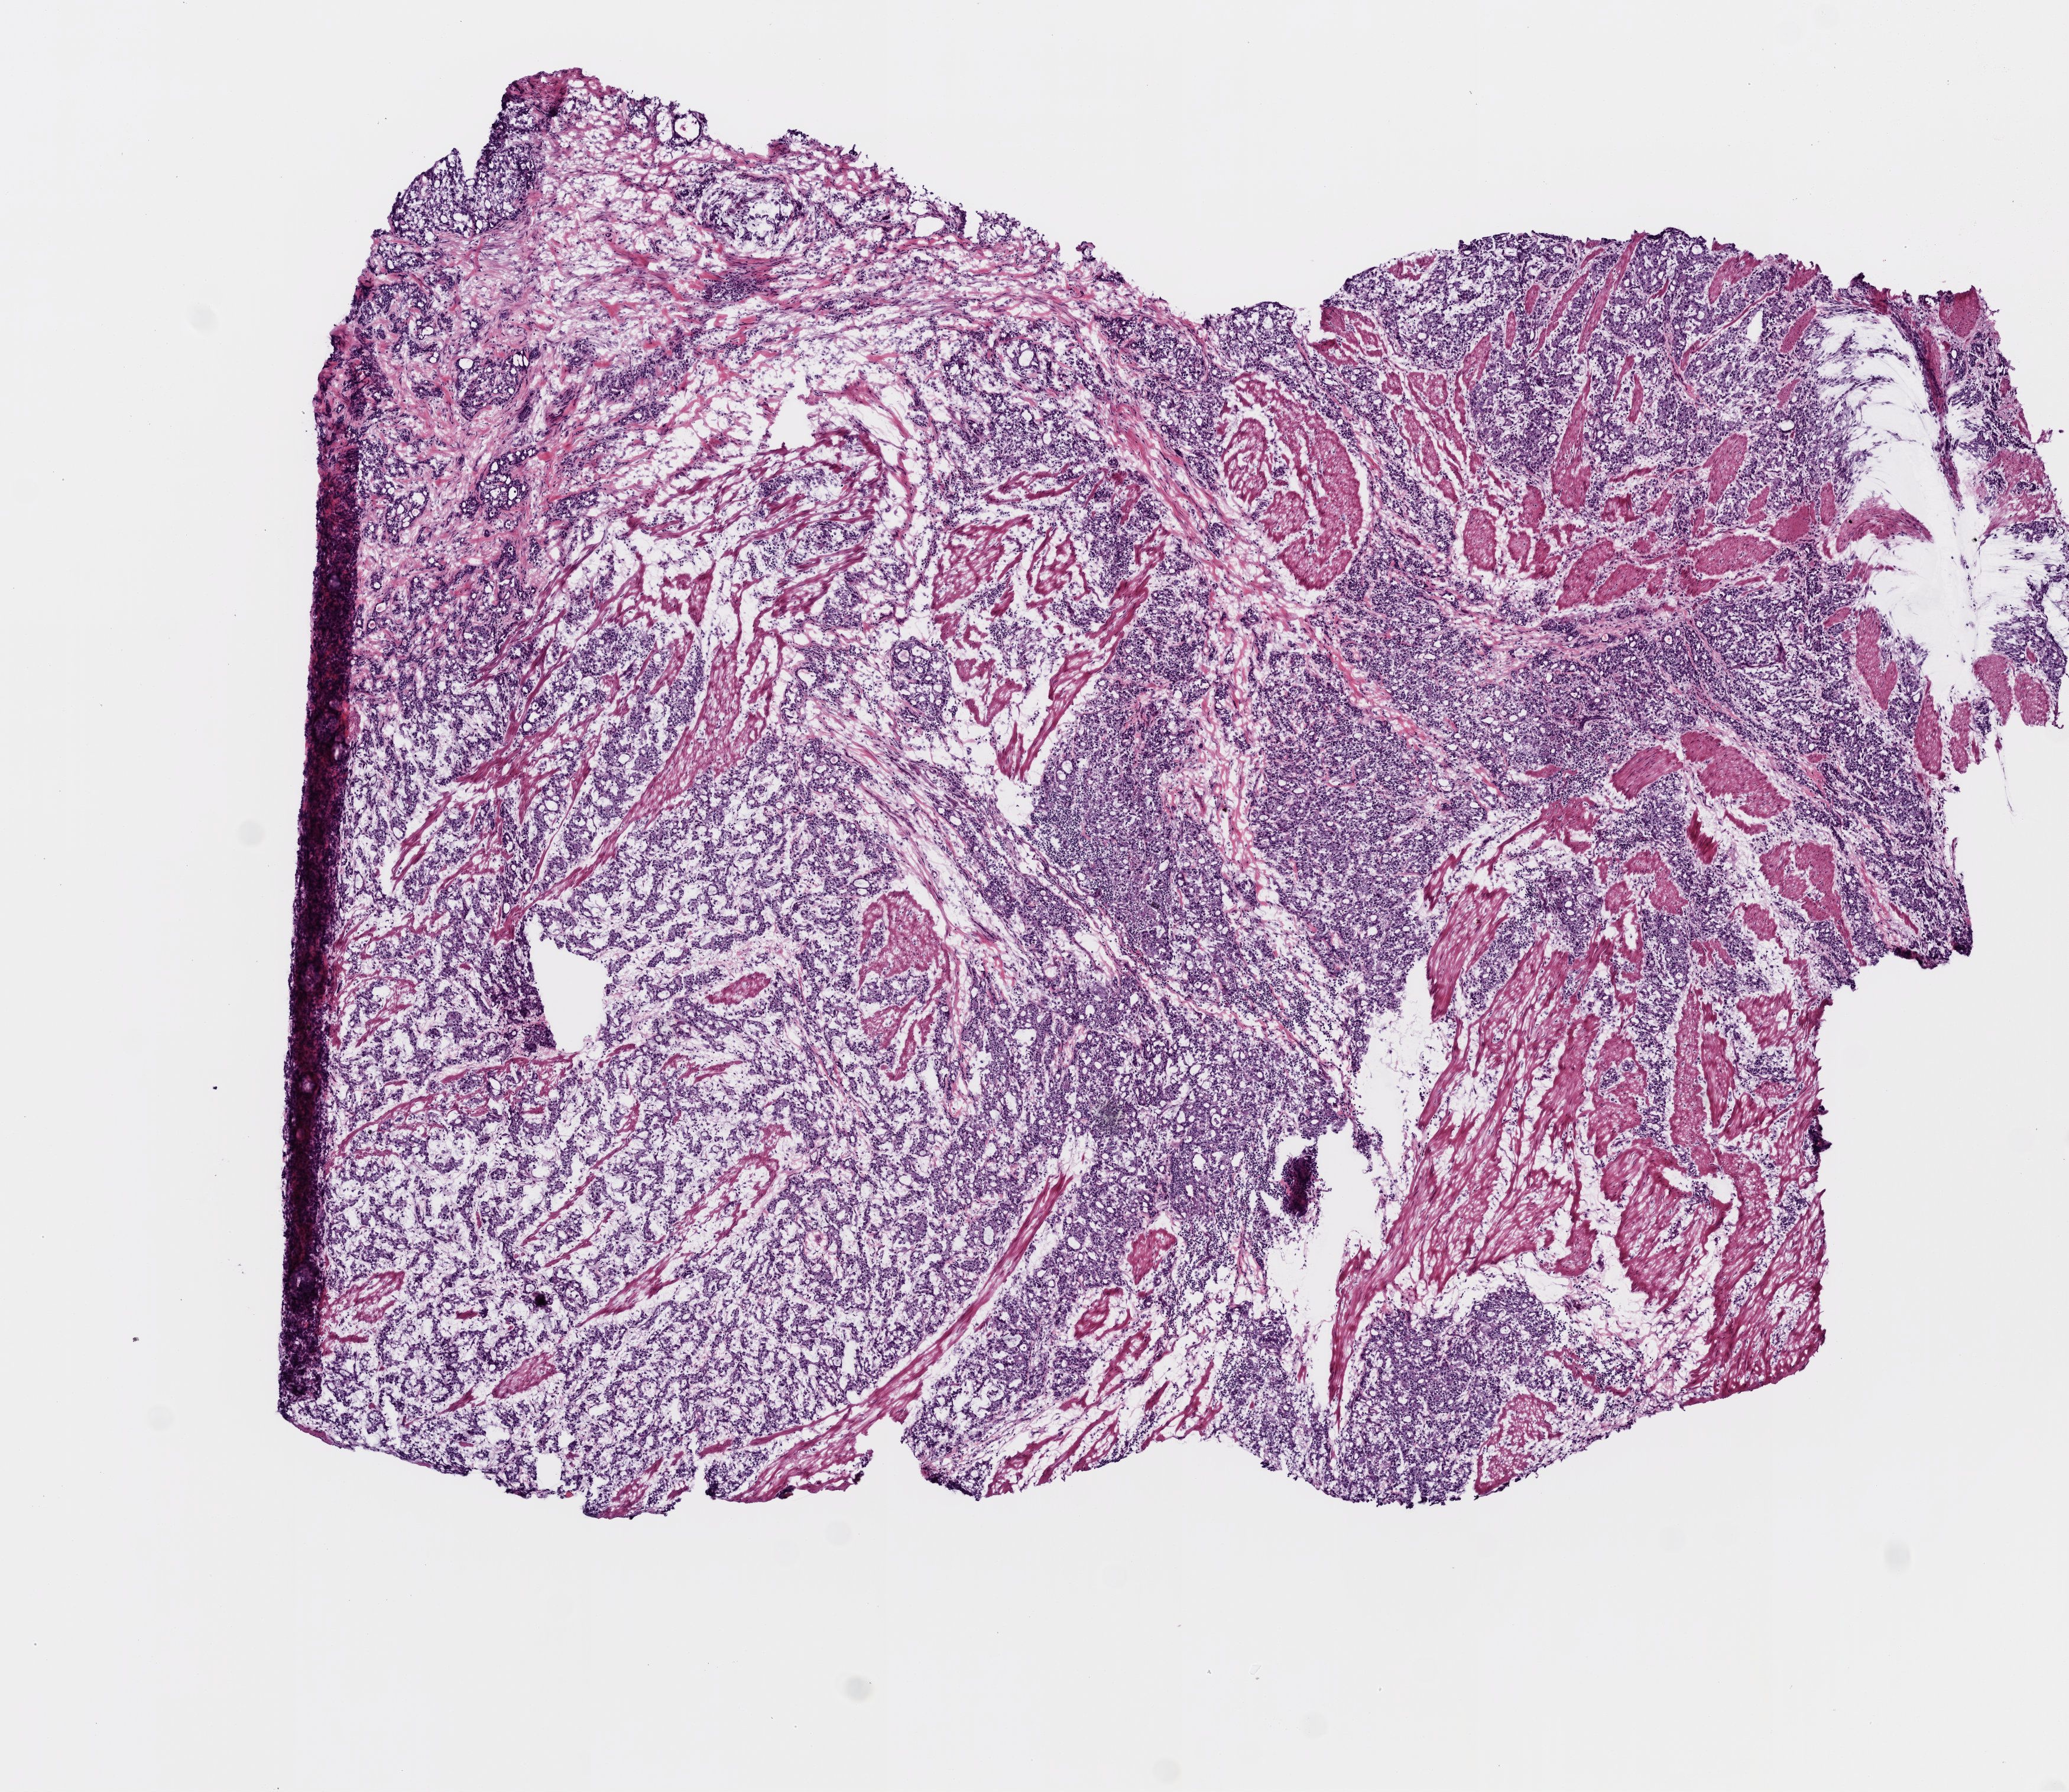
H&E-stained whole-slide image — whole scanned area (about 7.0 x 6.1 mm, from a 20x scan) shown as a low-resolution overview. Frozen section from the top of the tissue portion. Stomach, primary tumour sample. Male patient; age at initial diagnosis 49 years. Histologic grade: G3 (poorly differentiated). Slide review estimates, as recorded: tumour cells 88%, tumour nuclei 75%, normal cells 0%, stromal cells 10%, necrosis 2%.
Pathologic diagnosis: Adenocarcinoma with mixed subtypes (gastric antrum). TNM: T4 N1 M0. AJCC pathologic stage: IV (6th edition).